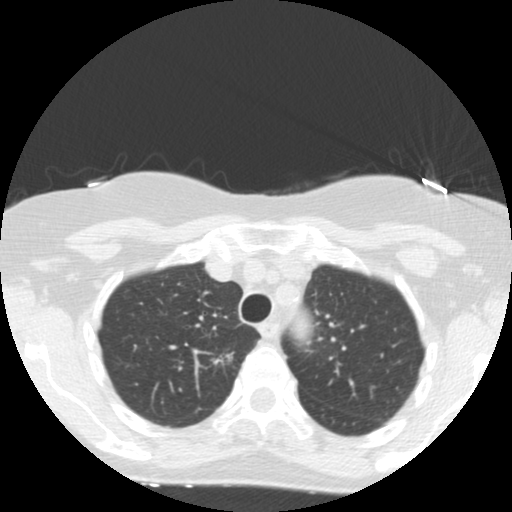
Chest CT (low-dose screening protocol), one axial image. Baseline annual screen. Lung window (W 1500 / L -600 HU). 2.5 mm slice thickness. Standard (soft-tissue) reconstruction kernel (STANDARD). 512 × 512 image matrix, field of view 300 × 300 mm. Female, age 67 years at enrolment. Former smoker at enrolment.
Lesion marked by an expert reader, box from (x=194, y=341) to (x=255, y=386) px. The exam's reader record, not a measurement of the box and not confirmed to be the same lesion: non-calcified nodule or mass ≥4 mm, right upper lobe, 16 × 7 mm, poorly defined margins, mixed attenuation. Participant outcome: lung cancer diagnosed 132 days after this screen — adenocarcinoma, NOS, right upper lobe, moderately differentiated (G2), stage IA (AJCC 6th edition), 13 mm at pathology.